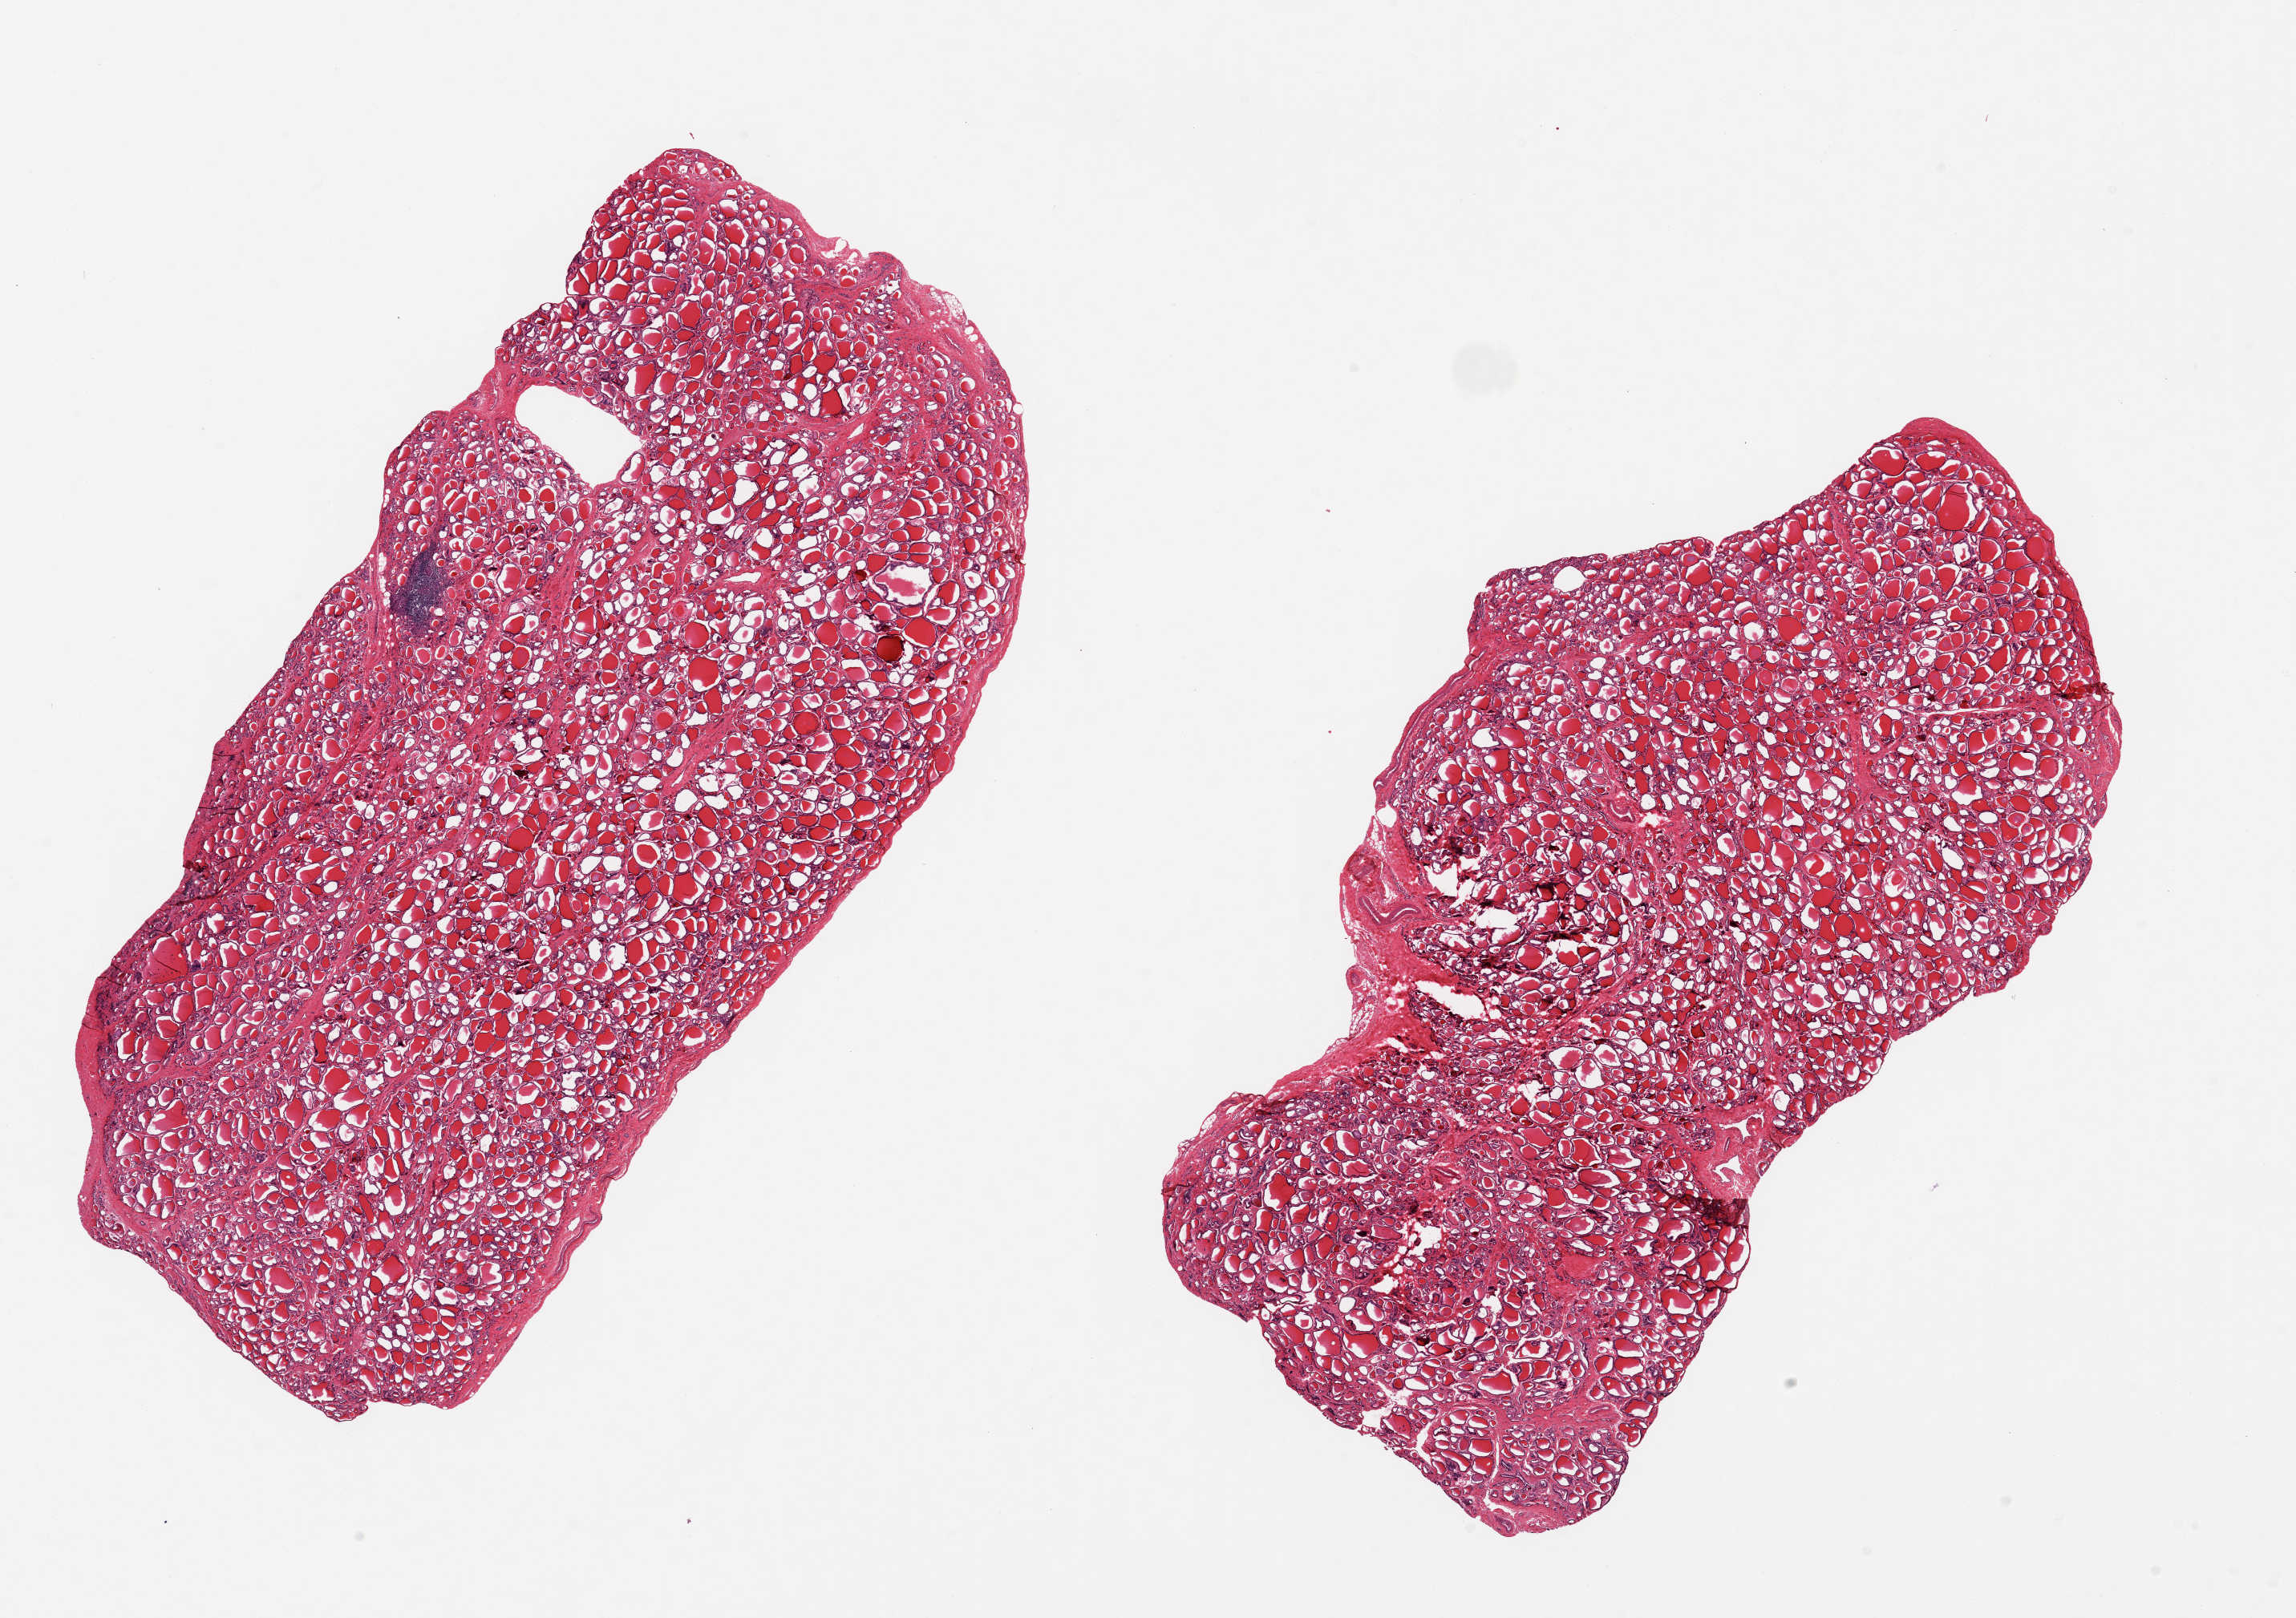
Whole-slide image, haematoxylin and eosin stain, brightfield, low-resolution overview of the scanned area, about 22.6 x 16.0 mm (slide scanned at 20x). PAXgene-fixed paraffin-embedded (PFPE) section. Sampled site (target tissue): thyroid. Tissue donor sample.
* review note (as recorded): 2 pieces, ~12x6mm; Focal lymphocytic thyroiditis, not diffuse enough to be Hashimoto's